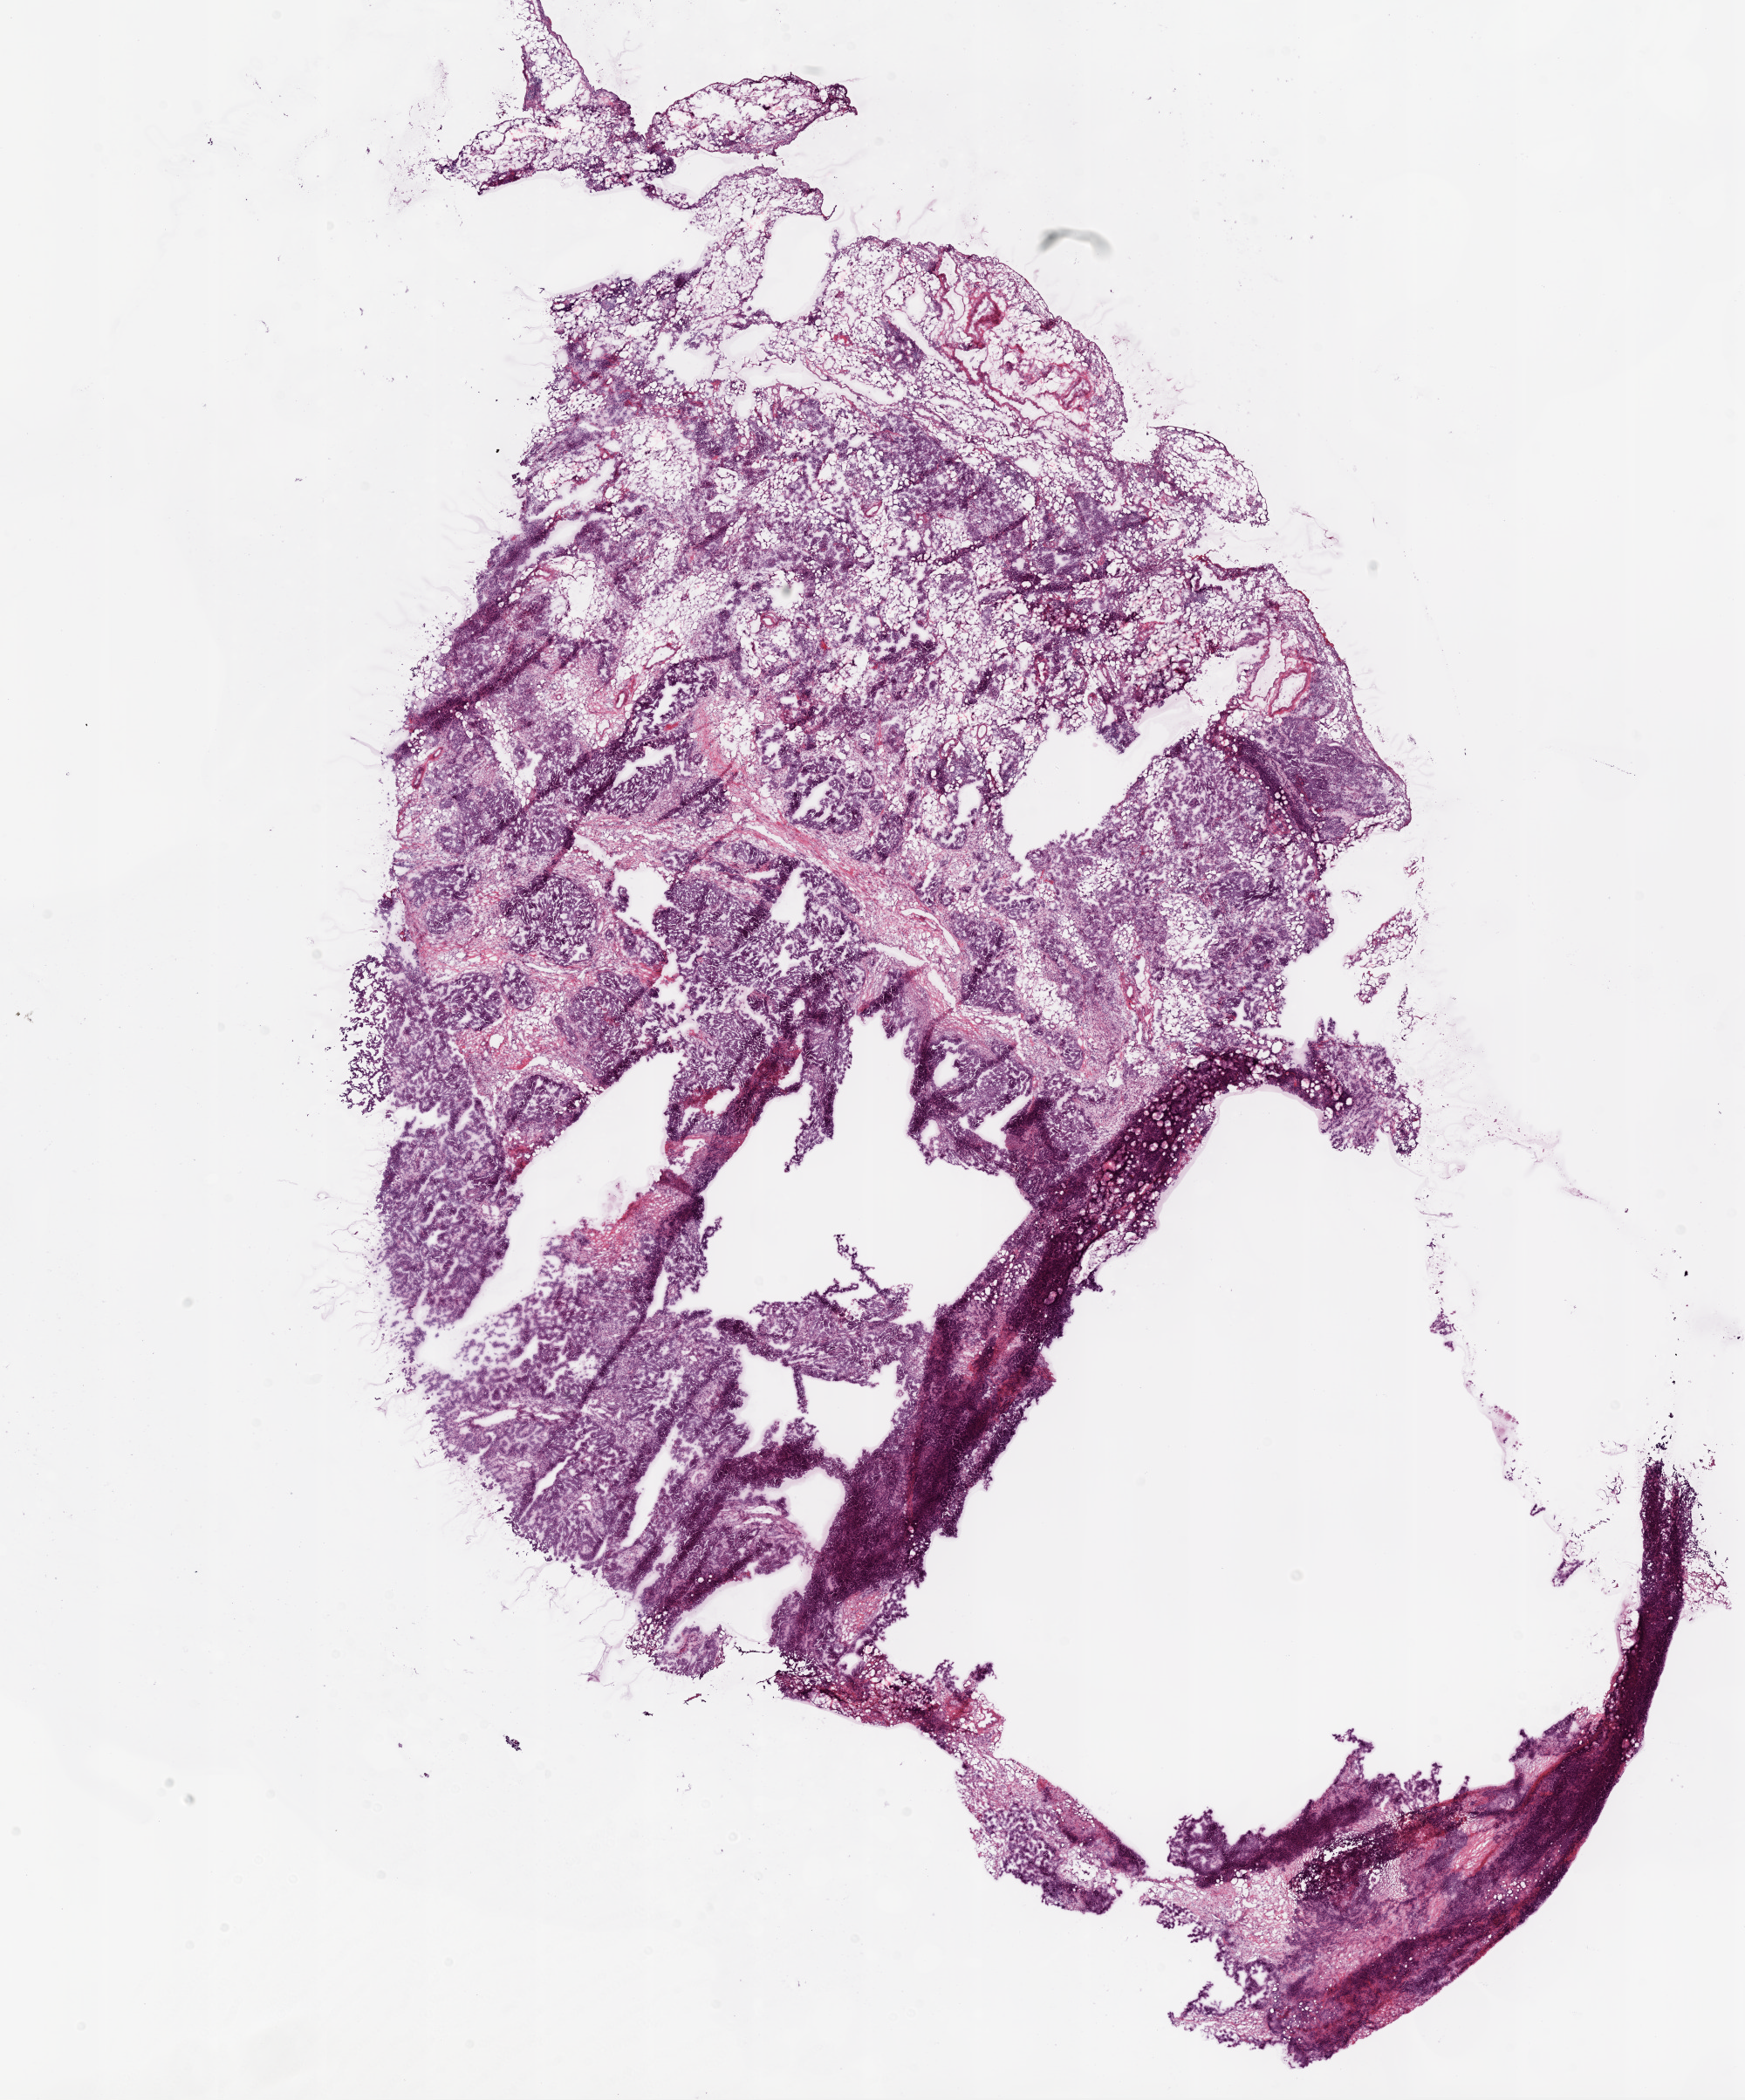
Digitized H&E tissue section (whole slide), low-resolution overview of the scanned area, about 16.0 x 19.3 mm; frozen section; primary tumour sample from the ovary. Female patient; age at initial diagnosis 50 years. Histologic grade: G3 (poorly differentiated). Composition of this section per pathologist review: tumour cells 60%, tumour nuclei 70%, normal cells 0%, stromal cells 40%, necrosis 0%.
Laterality: bilateral. FIGO stage: IV. Histologic diagnosis: Serous cystadenocarcinoma, NOS.